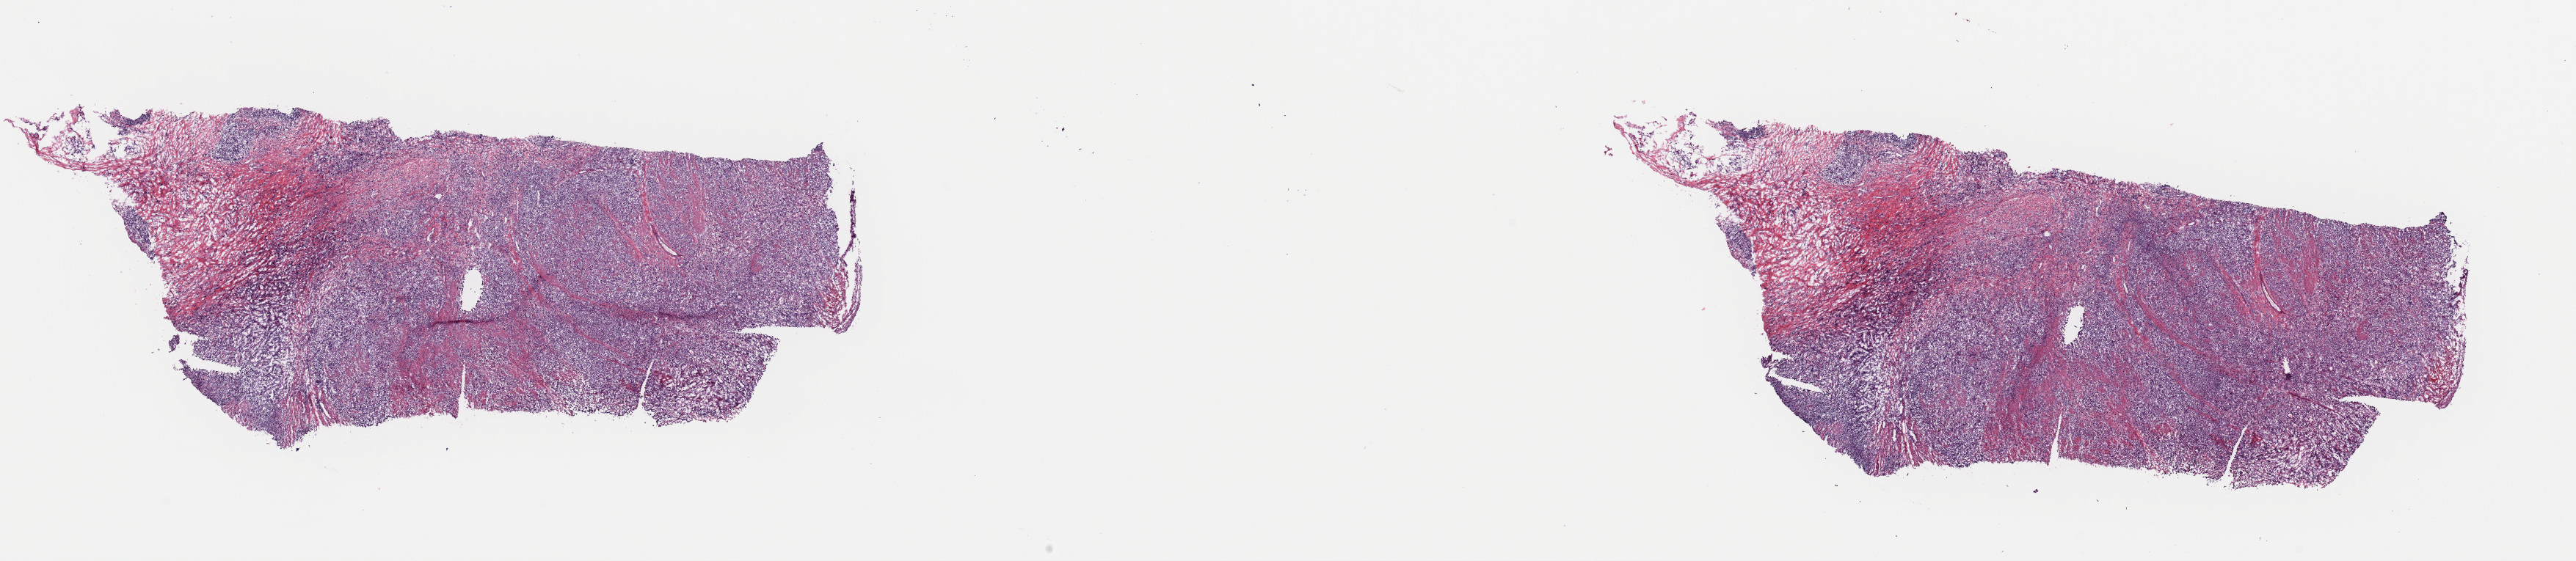
Digitized H&E tissue section (whole slide) — shown as a low-resolution overview of the whole scanned area (about 27.7 x 6.0 mm); frozen section; esophagus, primary tumour sample. Patient: female, age at initial diagnosis 50 years. Histologic grade: G2 (moderately differentiated). Composition of this section per pathologist review: tumour cells 62%, tumour nuclei 65%, normal cells 0%, stromal cells 35%, necrosis 3%. Infiltration values recorded for this section: lymphocyte infiltration 30%, monocyte infiltration 1%, neutrophil infiltration 2%.
Histologic diagnosis: Adenocarcinoma, NOS (lower third of esophagus). AJCC pathologic stage: IIIA.